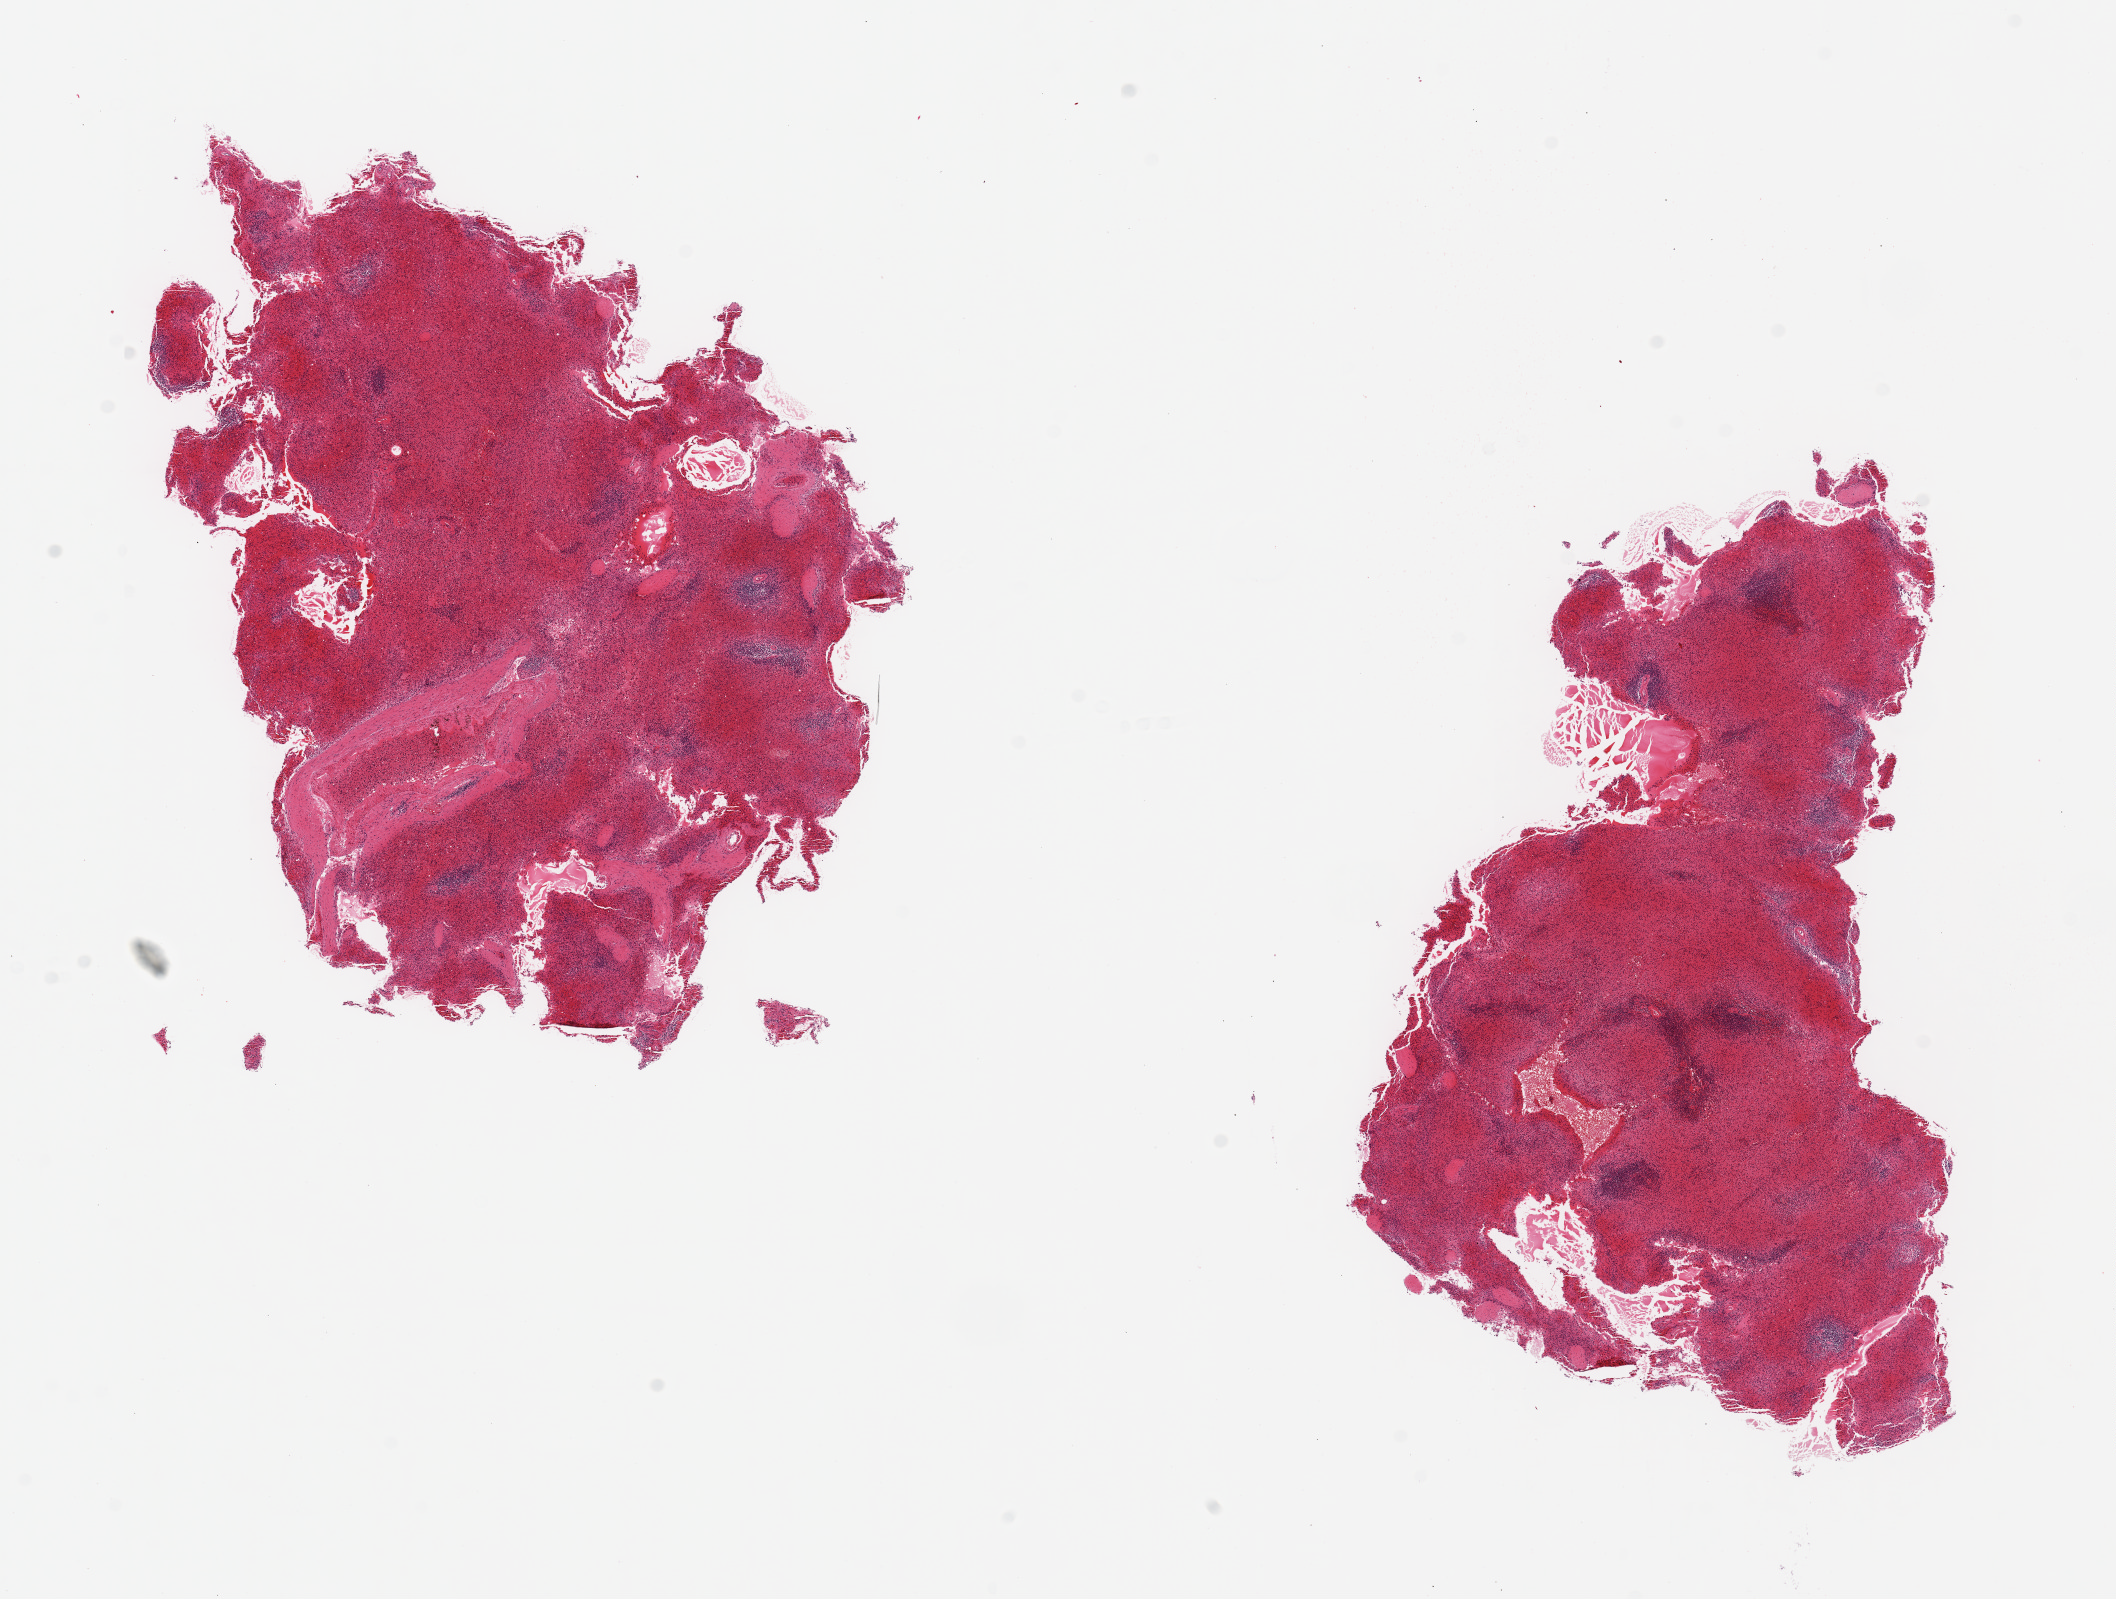
Haematoxylin and eosin whole-slide image, brightfield, whole scanned area (about 16.7 x 12.6 mm) shown as a low-resolution overview; PAXgene-fixed, paraffin-embedded tissue; target tissue: spleen; donor tissue sample. Male donor.
Reviewer comment on this tissue sample: 2 pieces, 9x7 & 8x5mm; moderate congestion.